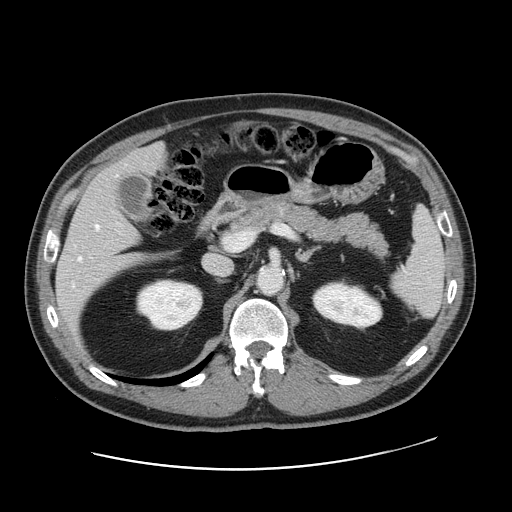
Contrast-enhanced abdominal CT, one axial slice. Position 91 of 178 along the scan axis. 120 kVp. Intravenous contrast given. Soft-tissue window (W 400 / L 40 HU). 512 × 512 image matrix, field of view 403 × 403 mm. Male patient, age 63 years. From the clinical record (not read from this slice): diagnosis: colorectal cancer liver metastases, imaged before liver resection; multiple liver metastases: yes; largest metastasis: 8 cm.
Outlined on this slice (expert manual segmentation):
- hepatic veins: bounding box <78,225,99,260> (left, top, right, bottom; pixels)
- liver: <57,145,166,328>
- planned liver remnant (the part of the liver to remain after resection): <116,145,166,176>
- portal vein (with intrahepatic branches): <224,232,255,251>